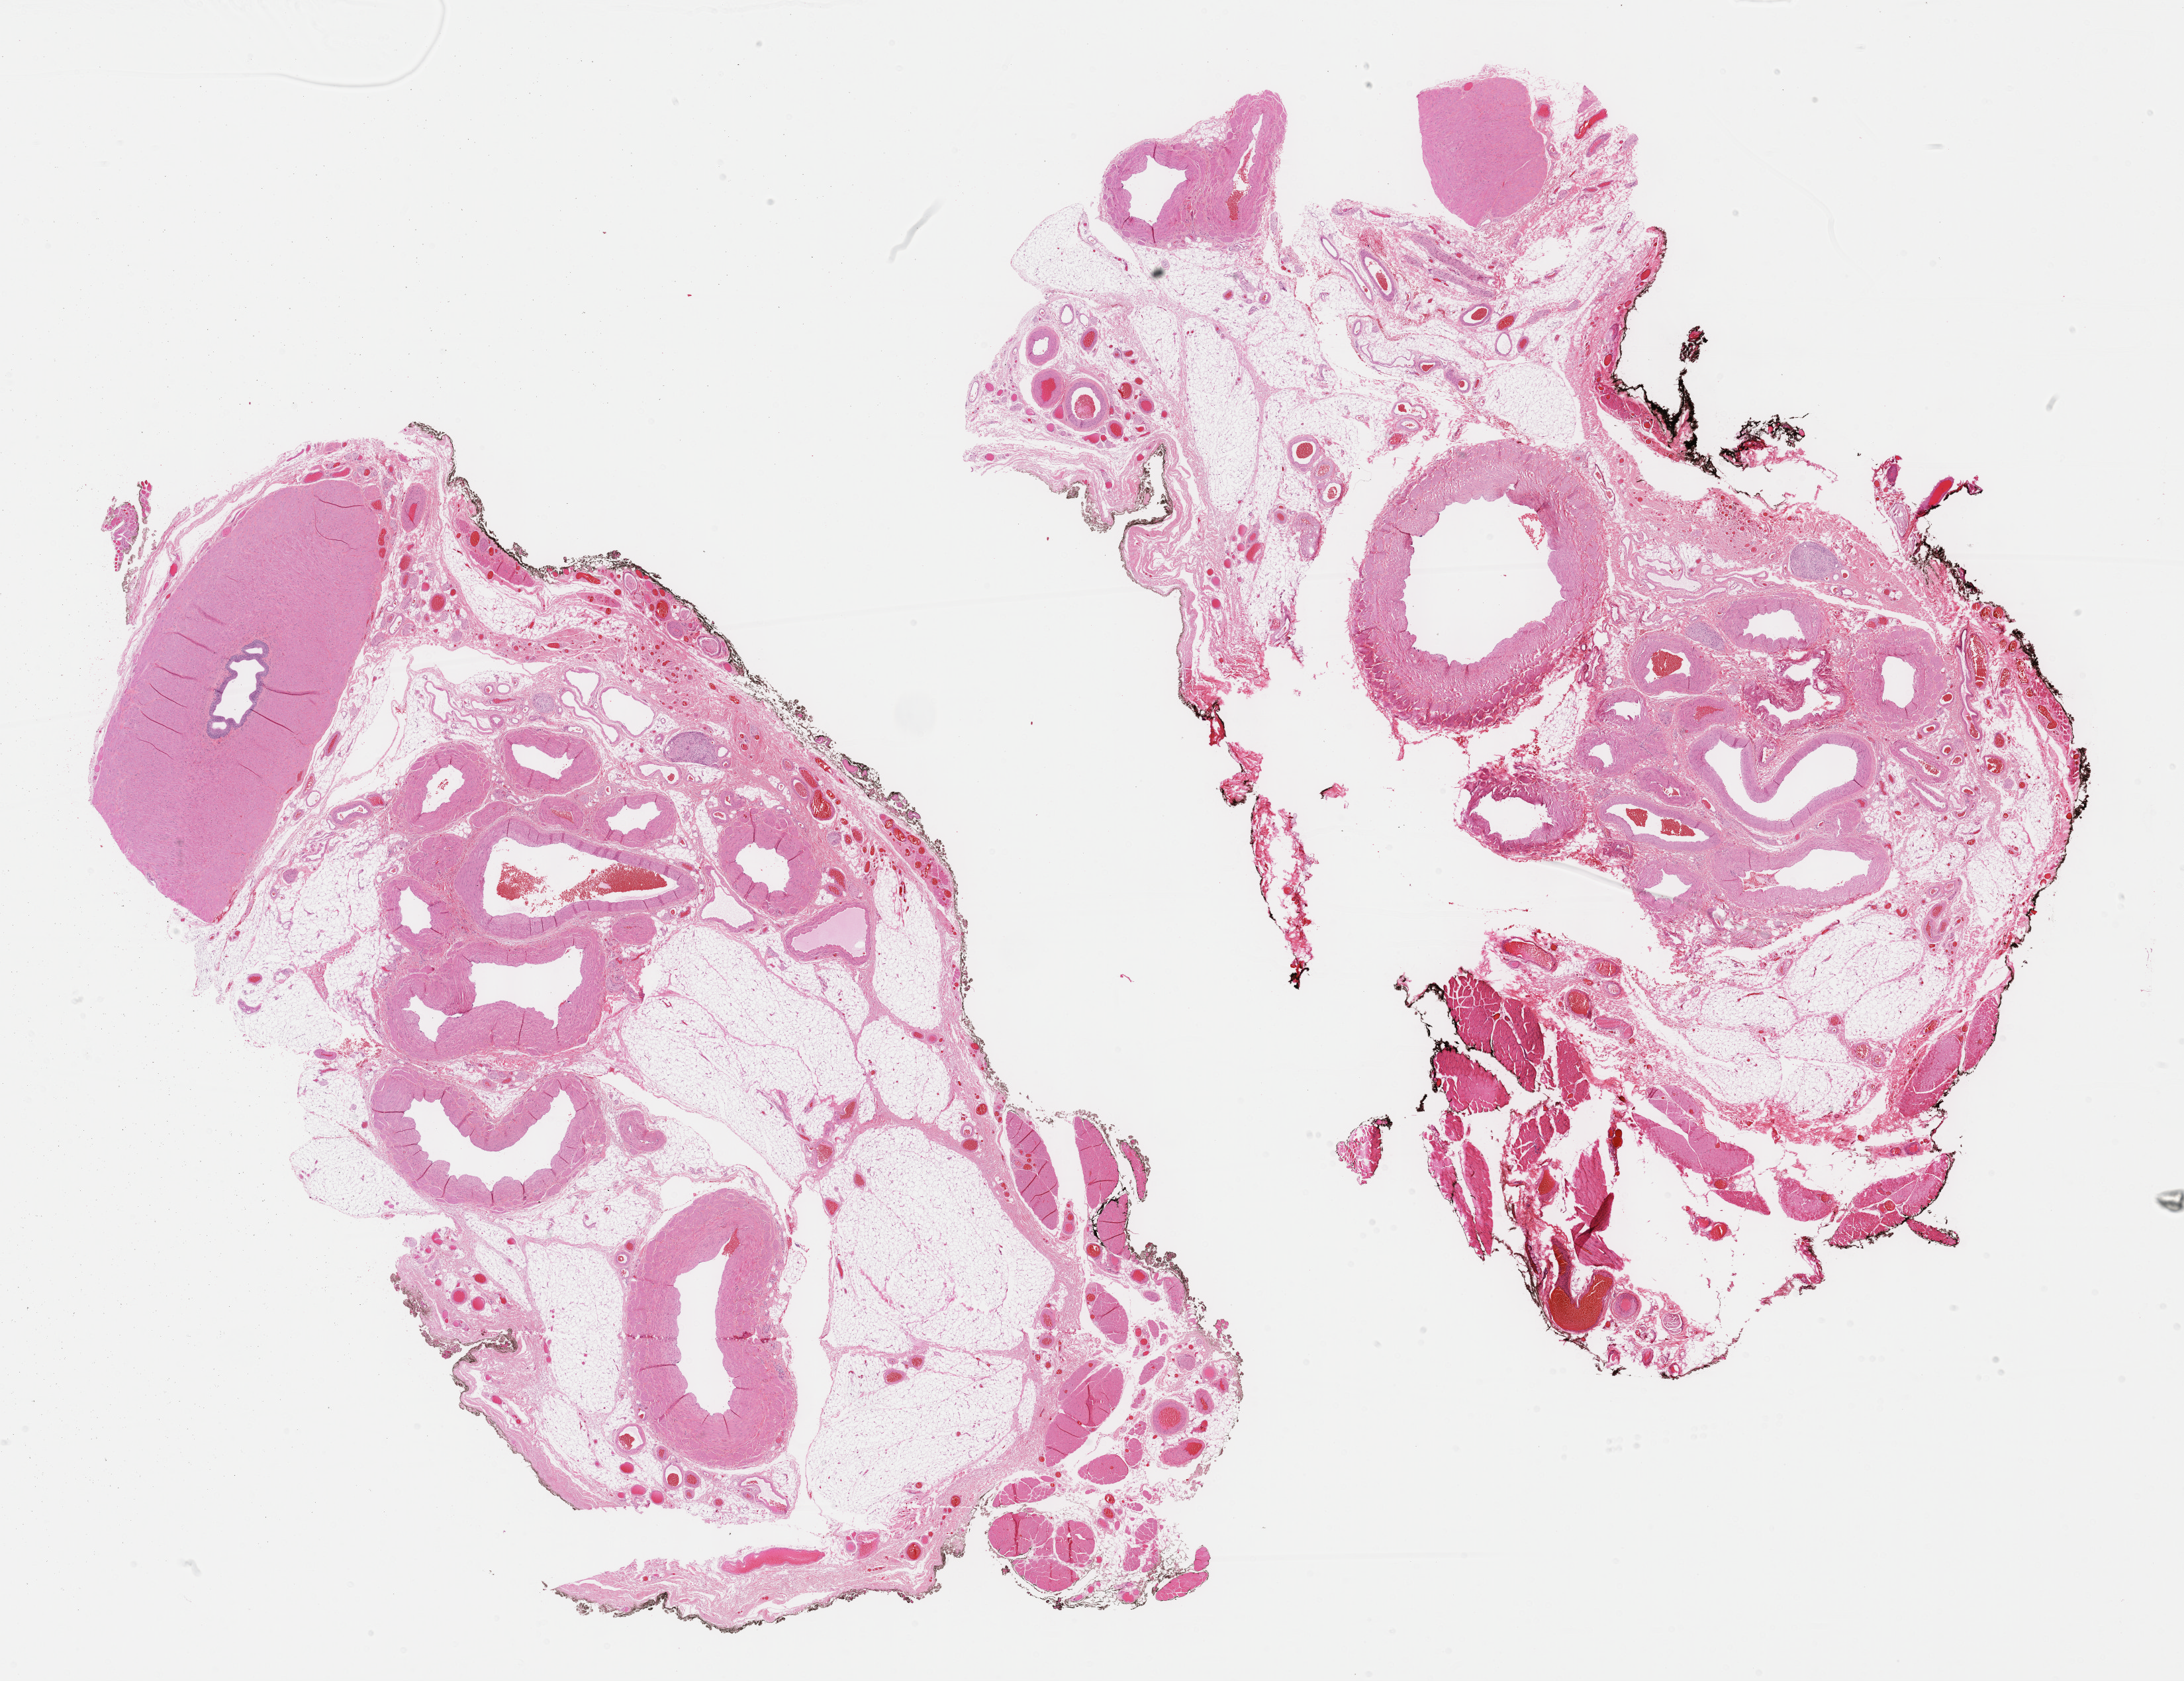
H&E whole-slide image — whole scanned area (about 26.7 x 20.5 mm) shown as a low-resolution overview, FFPE section, sample: primary tumour, testis. Male patient; age at initial diagnosis 38 years.
• histologic diagnosis: Seminoma, NOS
• laterality: left